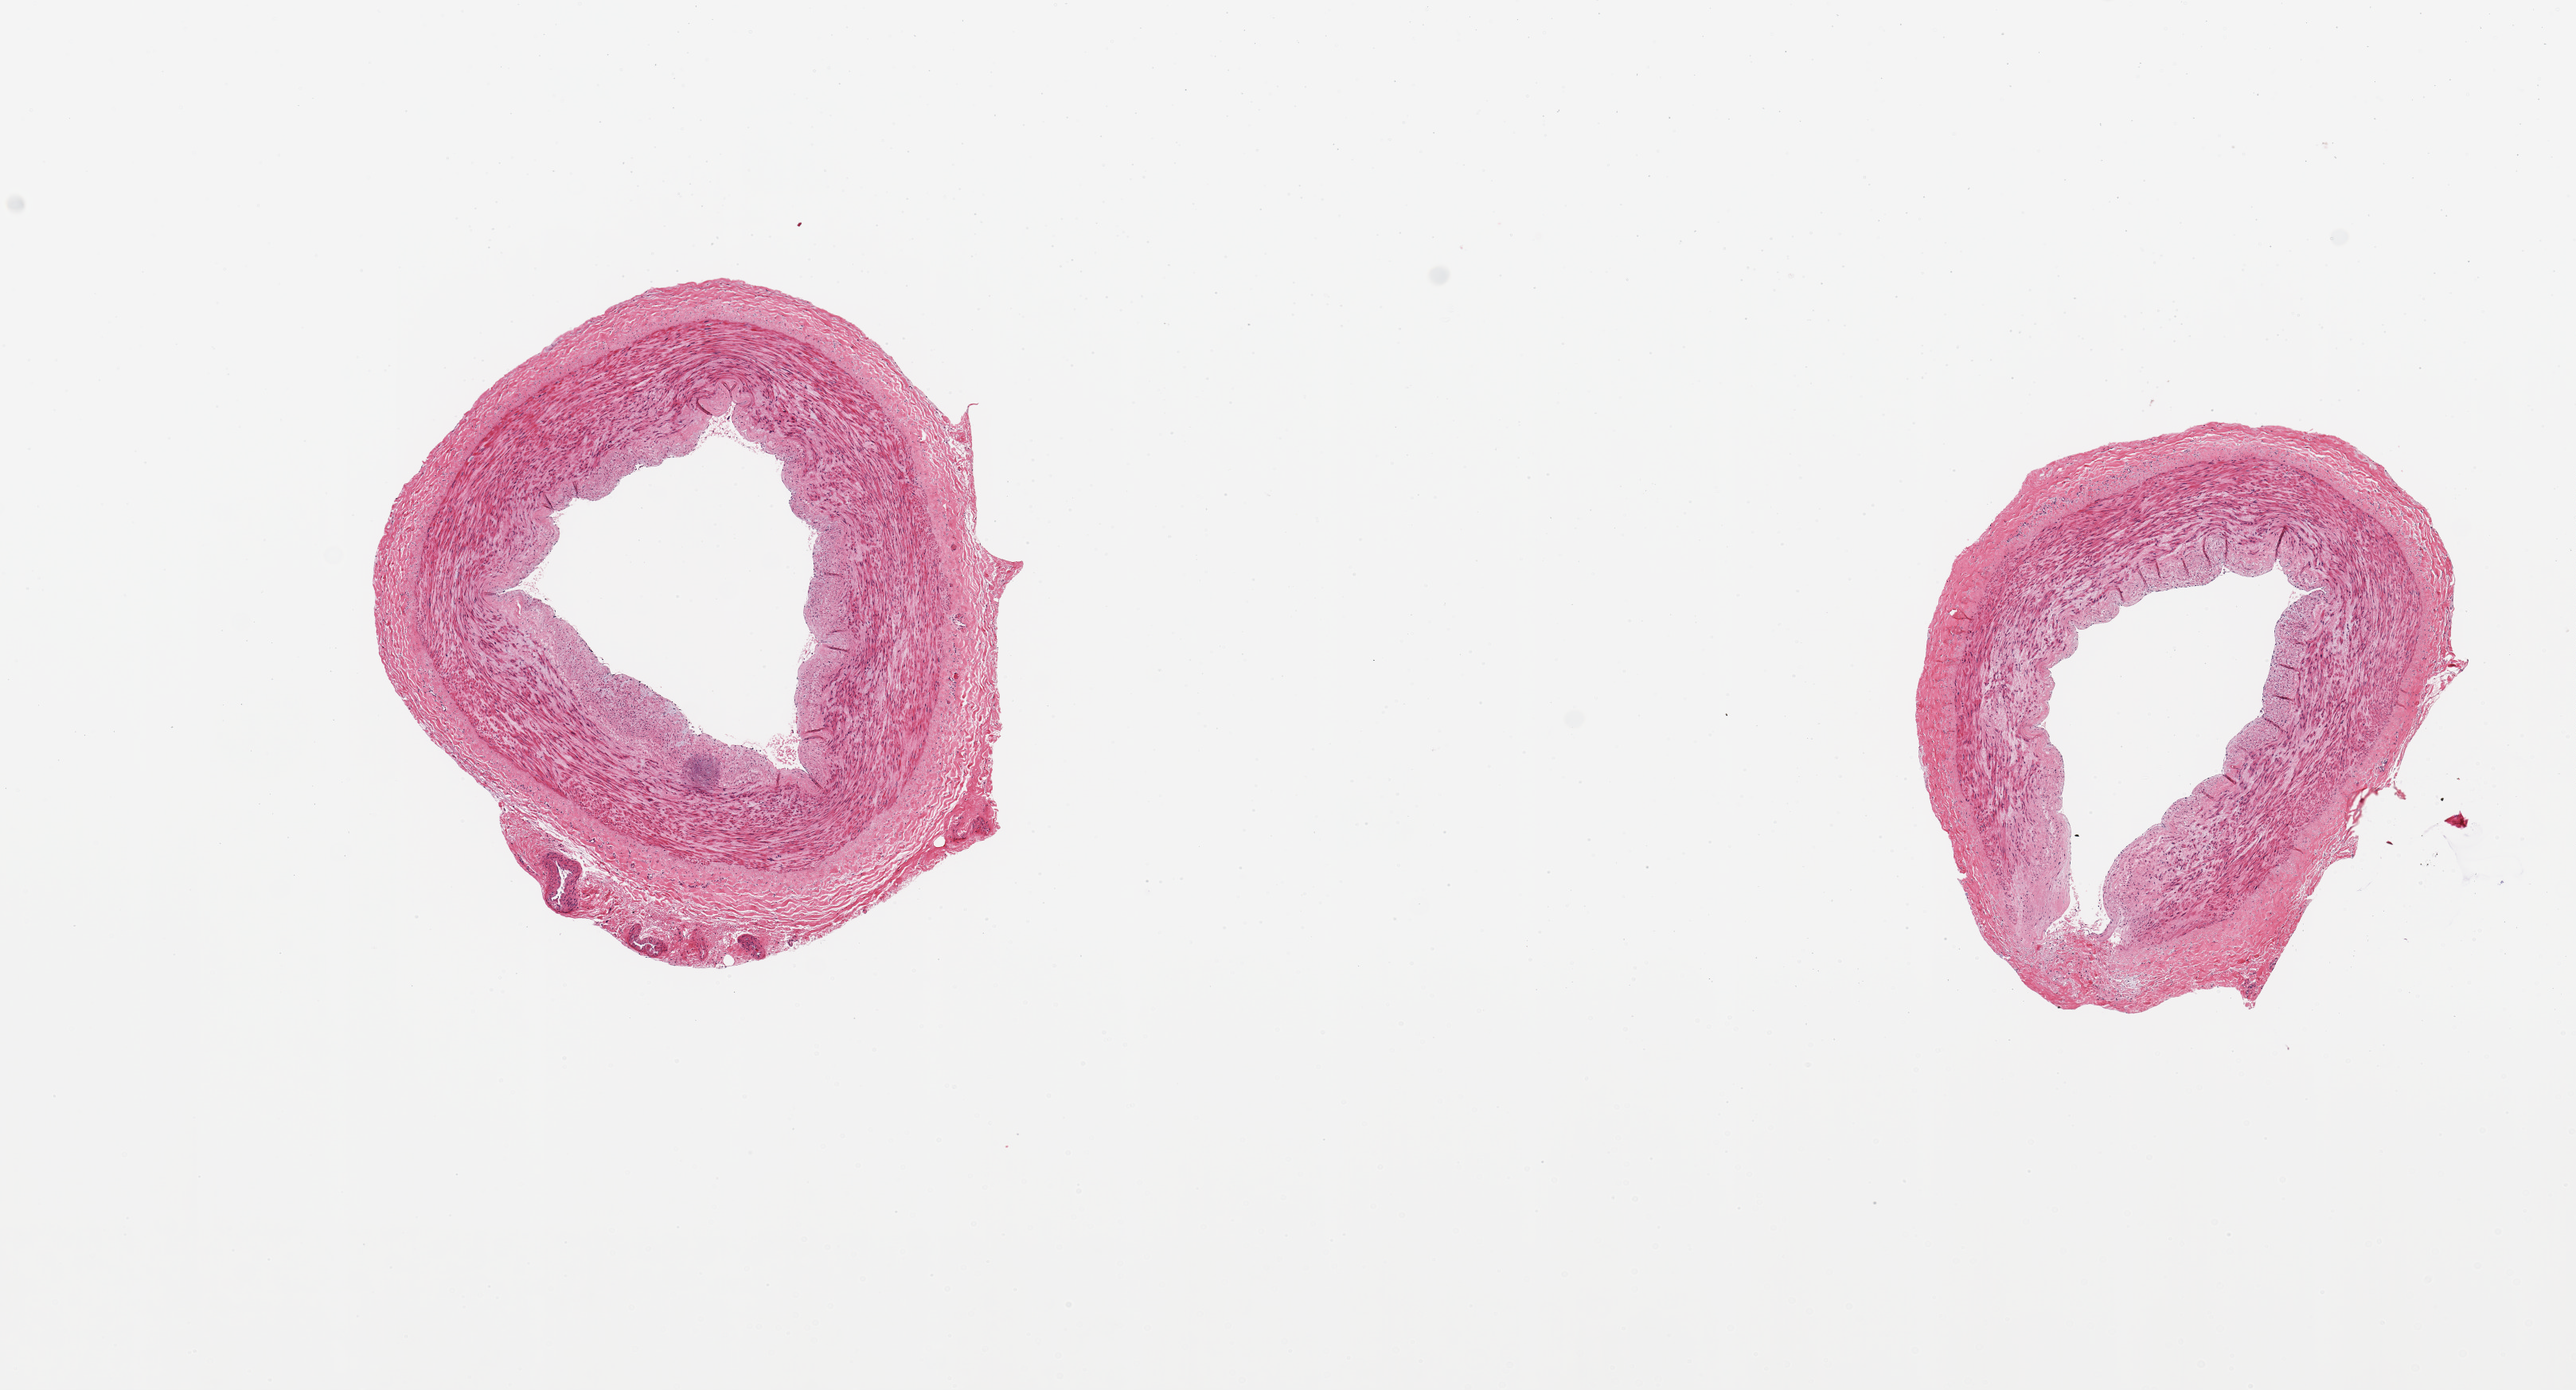
Digitized hematoxylin and eosin (H&E)-stained section — shown as a low-resolution overview of the whole scanned area (about 12.8 x 6.9 mm); PAXgene-fixed, paraffin-embedded tissue; section of tibial artery (target tissue); donor tissue sample. Donor: male.
Pathologist's review note for this sample: 2 pieces, ~2.5 mm diameter.